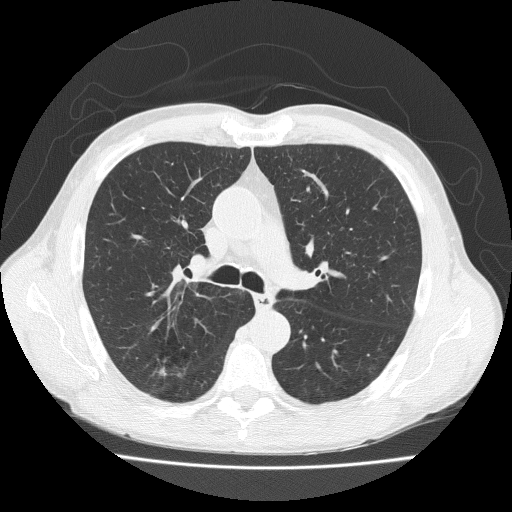
Chest CT (low-dose screening protocol), one axial image. Baseline screening round. Lung window (W 1500 / L -600 HU). 2 mm slice thickness. Lung (sharp) reconstruction kernel (FC51). Slice 74 of 203 in the series. 512 × 512 image matrix. Male participant, aged 73 years at enrolment. Current smoker at enrolment.
Expert-annotated lung lesion, box from (x=144, y=332) to (x=194, y=379) px. No non-calcified nodule or mass ≥4 mm was recorded by the screening reader at this exam. Official screen result: negative screen, no significant abnormalities. Later outcome: lung cancer diagnosed 777 days after this screen (after the third annual screen) — adenosquamous carcinoma, right upper lobe, well differentiated (G1), stage IA (AJCC 6th edition), 20 mm at pathology.